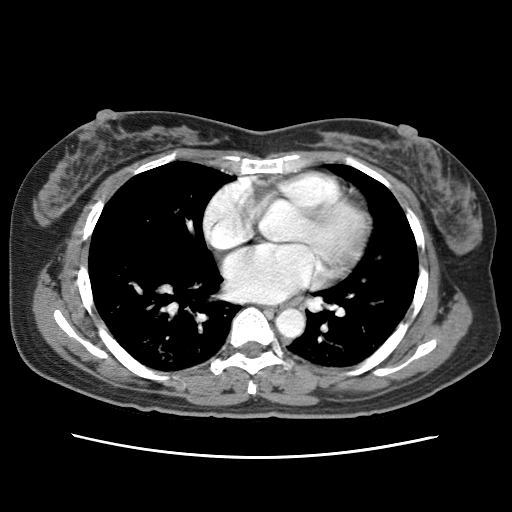
Contrast-enhanced abdominal CT (liver protocol), one axial slice; slice 77 of 79 in the series (ordered by position); reconstruction kernel STANDARD; 120 kVp; soft-tissue window (W 400 / L 40 HU); 2.5 mm slice thickness; 512 × 512 image matrix, field of view 340 × 340 mm. From the clinical record (not read from this slice): diagnosis: hepatocellular carcinoma (patient treated with transarterial chemoembolisation; whether this scan precedes or follows treatment is not stated here); TNM stage (as recorded): Stage-I; Child-Pugh class: A; tumour differentiation: moderately differentiated.
Outlined on this slice (semi-automatically segmented with operator editing):
- abdominal aorta: bounding box [x1, y1, x2, y2] px = [276, 308, 305, 338]